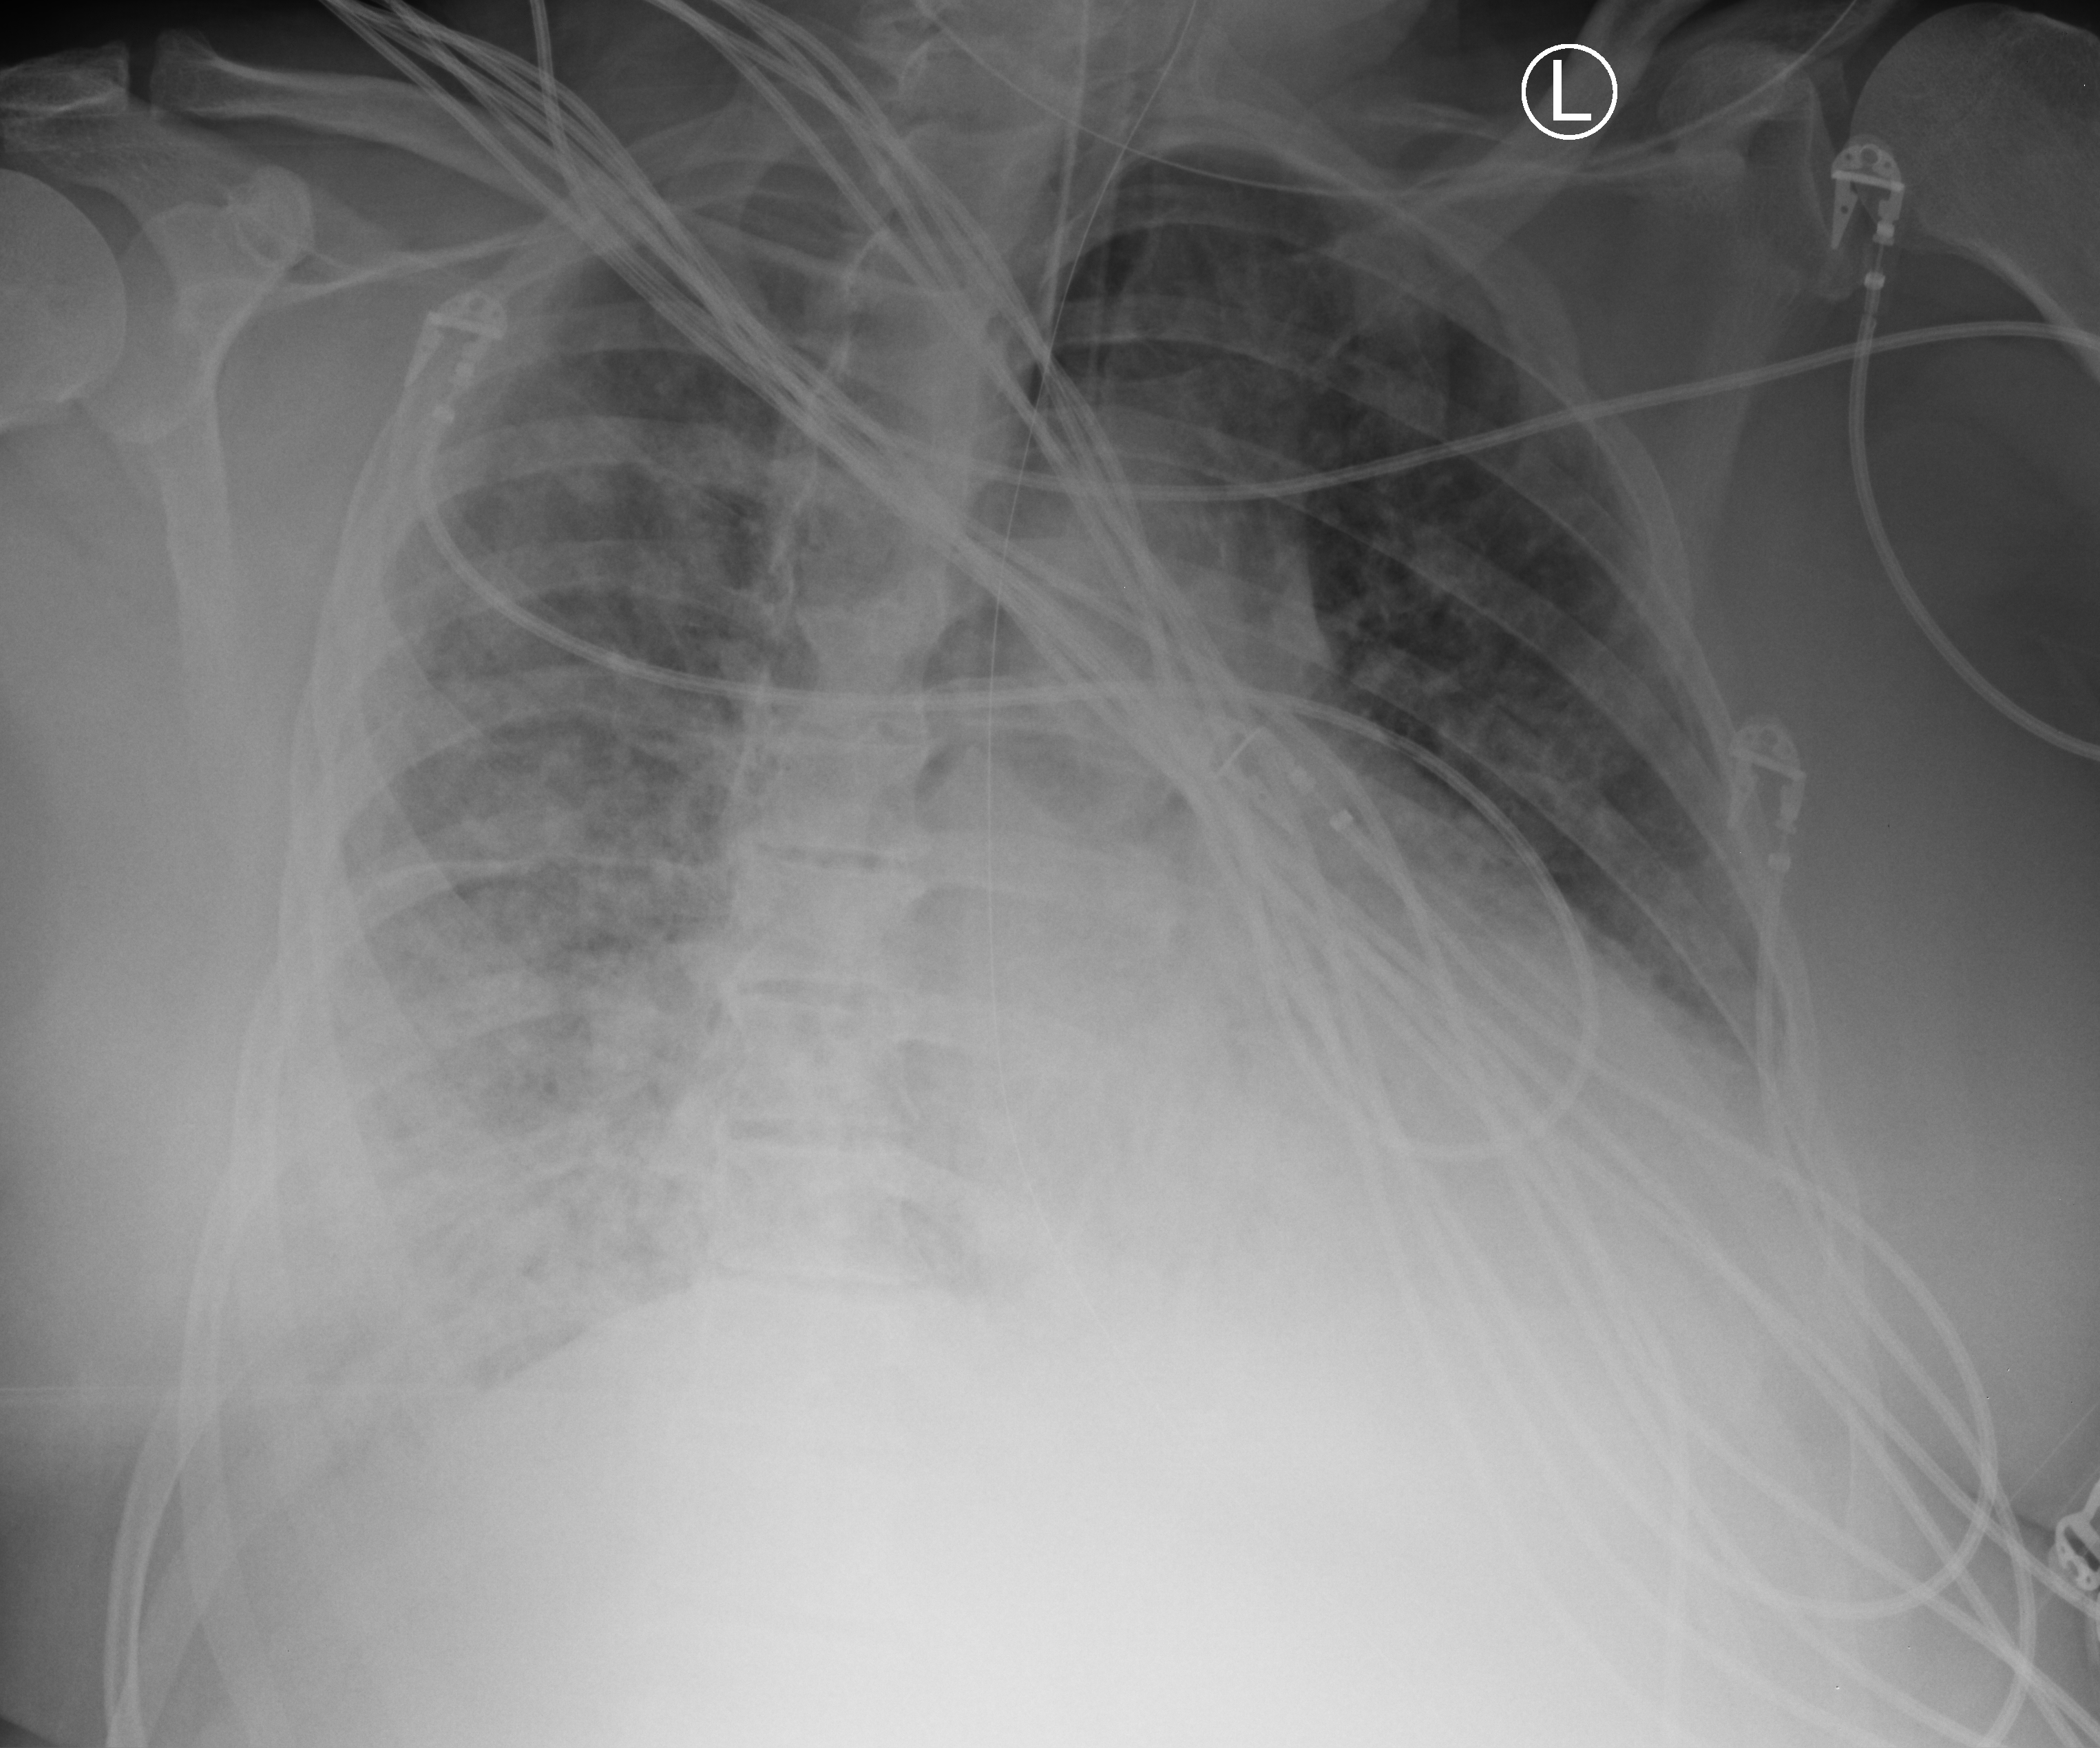
Bedside chest radiograph (computed radiography), anteroposterior (AP) projection. Male patient hospitalised with COVID-19, age 60–74 years.
Admission-level facts for this patient (not findings on this image; timing relative to this image not recorded): smoking status (admission record): former; admitted to intensive care during this hospital stay: yes.